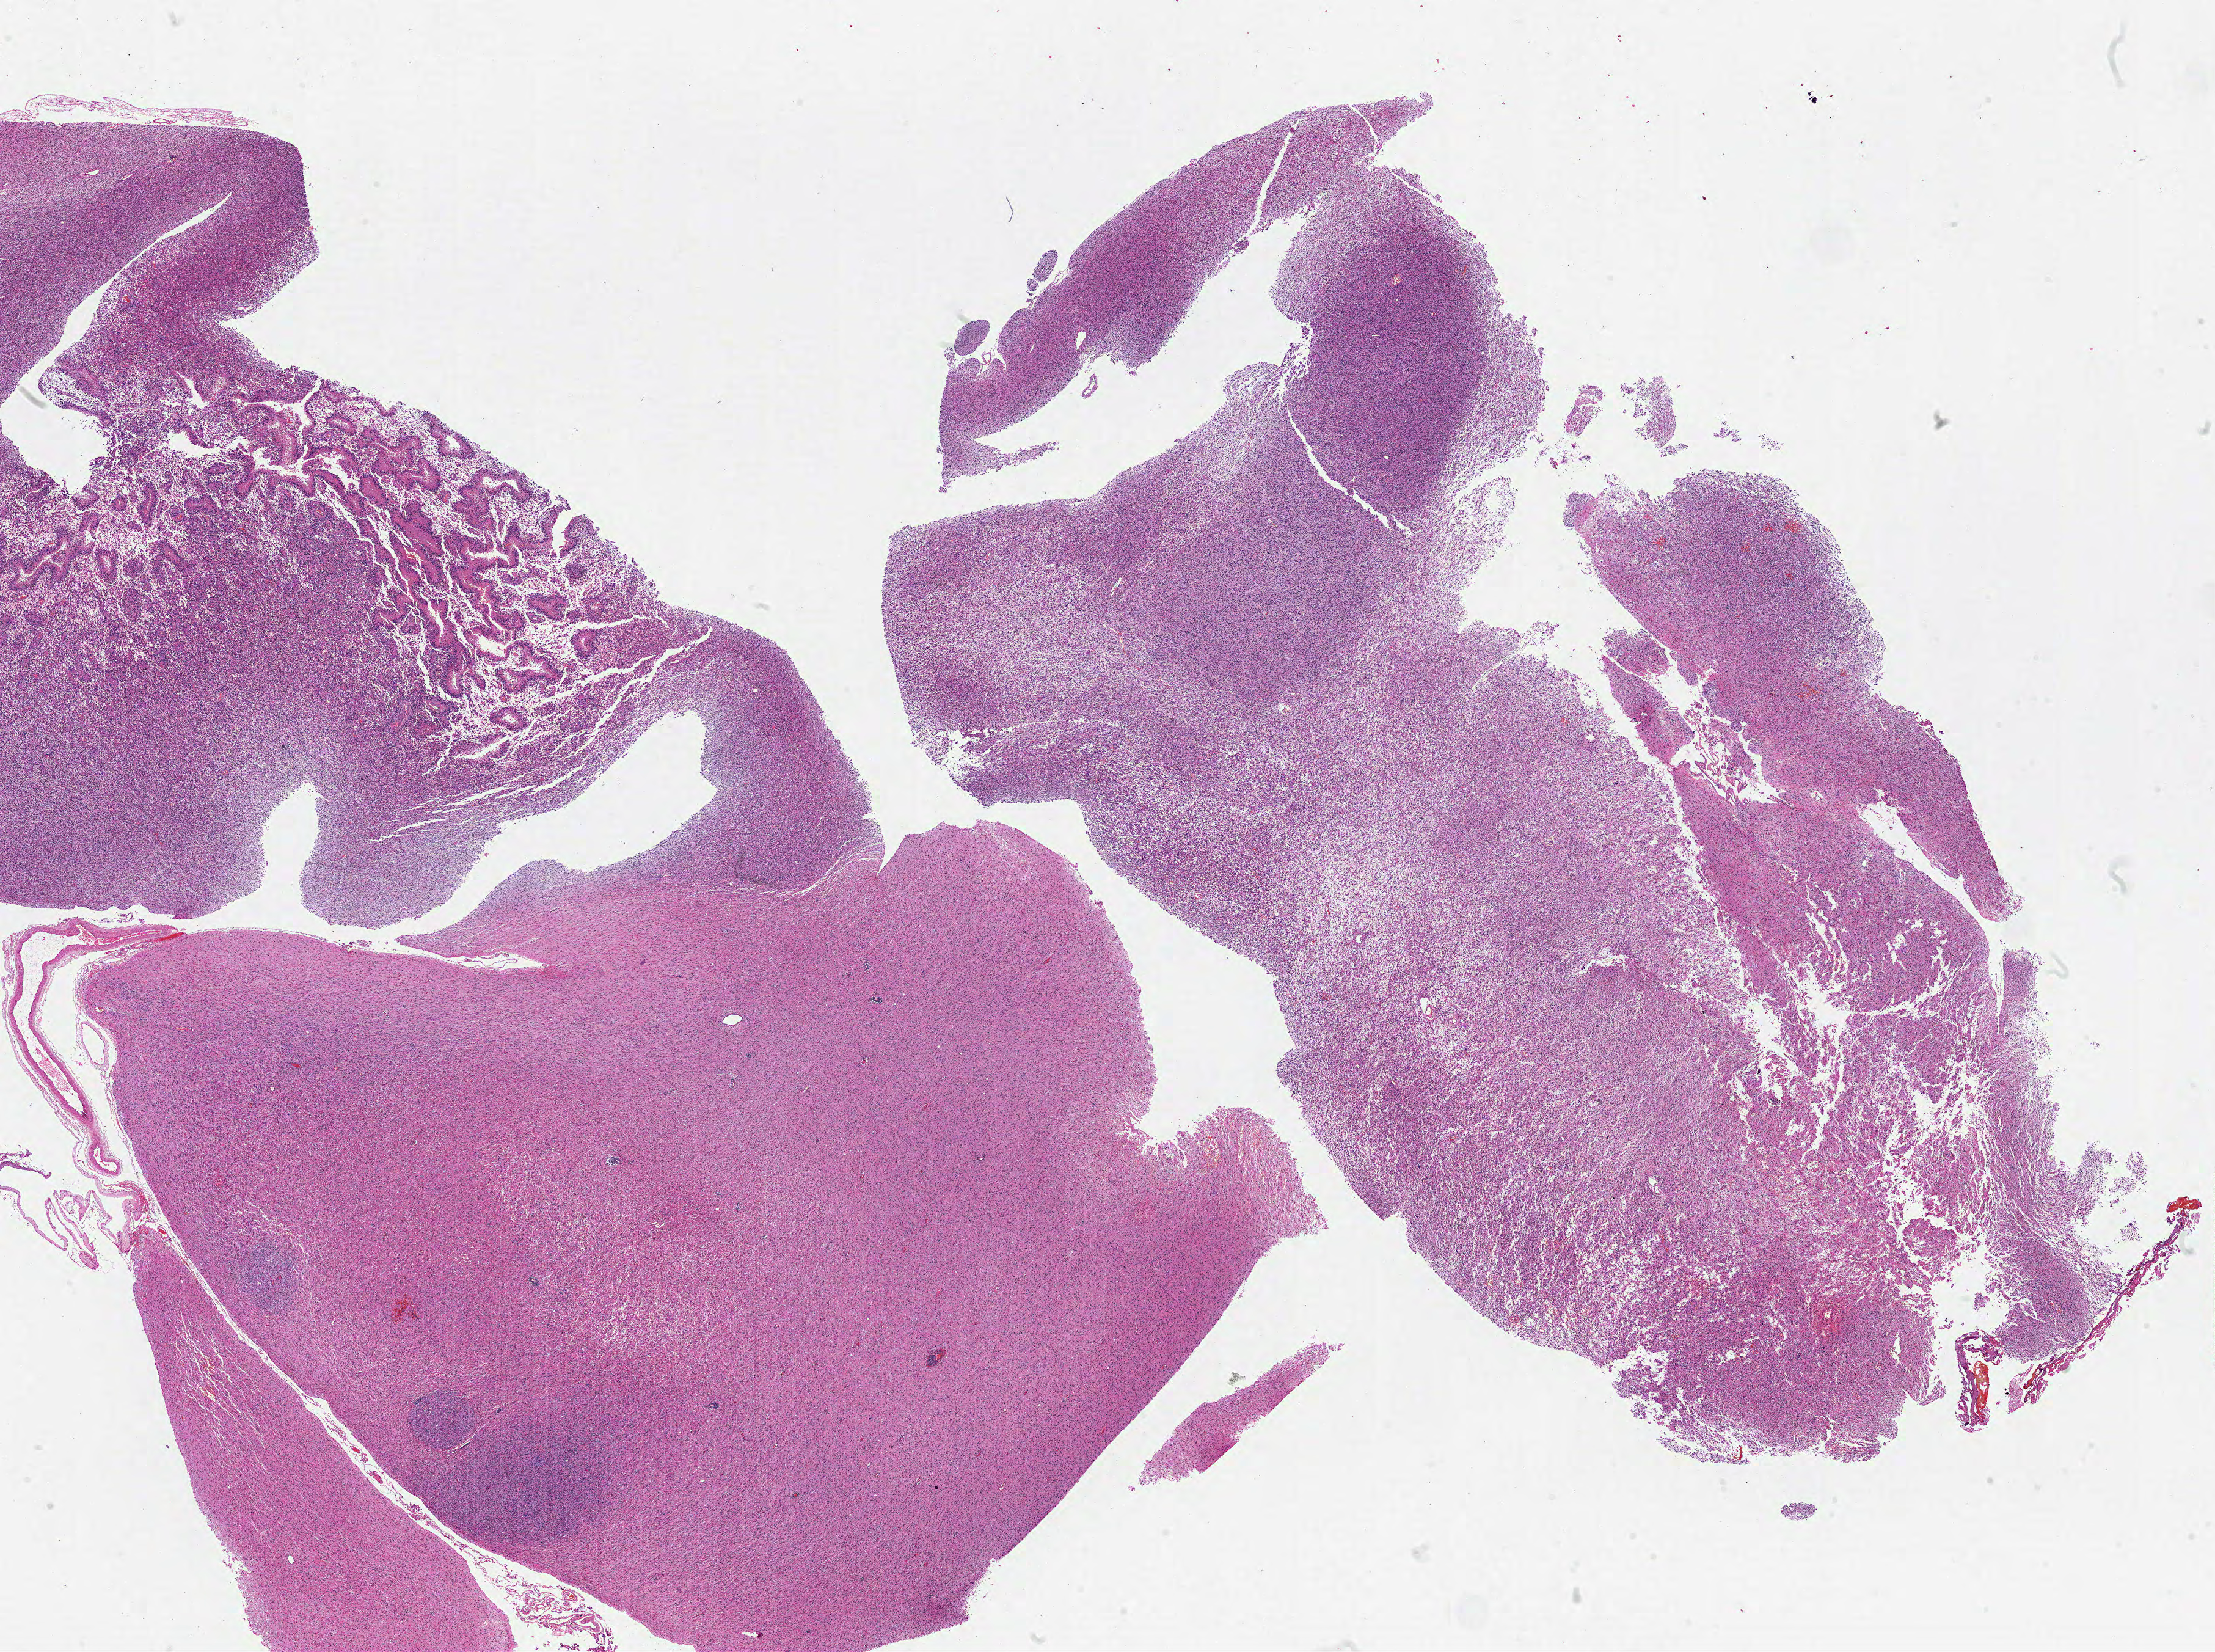
Whole-slide histology image, H&E-stained — low-resolution overview of the scanned area, about 29.0 x 21.6 mm (slide scanned at 20x); FFPE section; brain, primary tumour sample. Male patient; age at initial diagnosis 63 years.
Diagnosis: Glioblastoma.